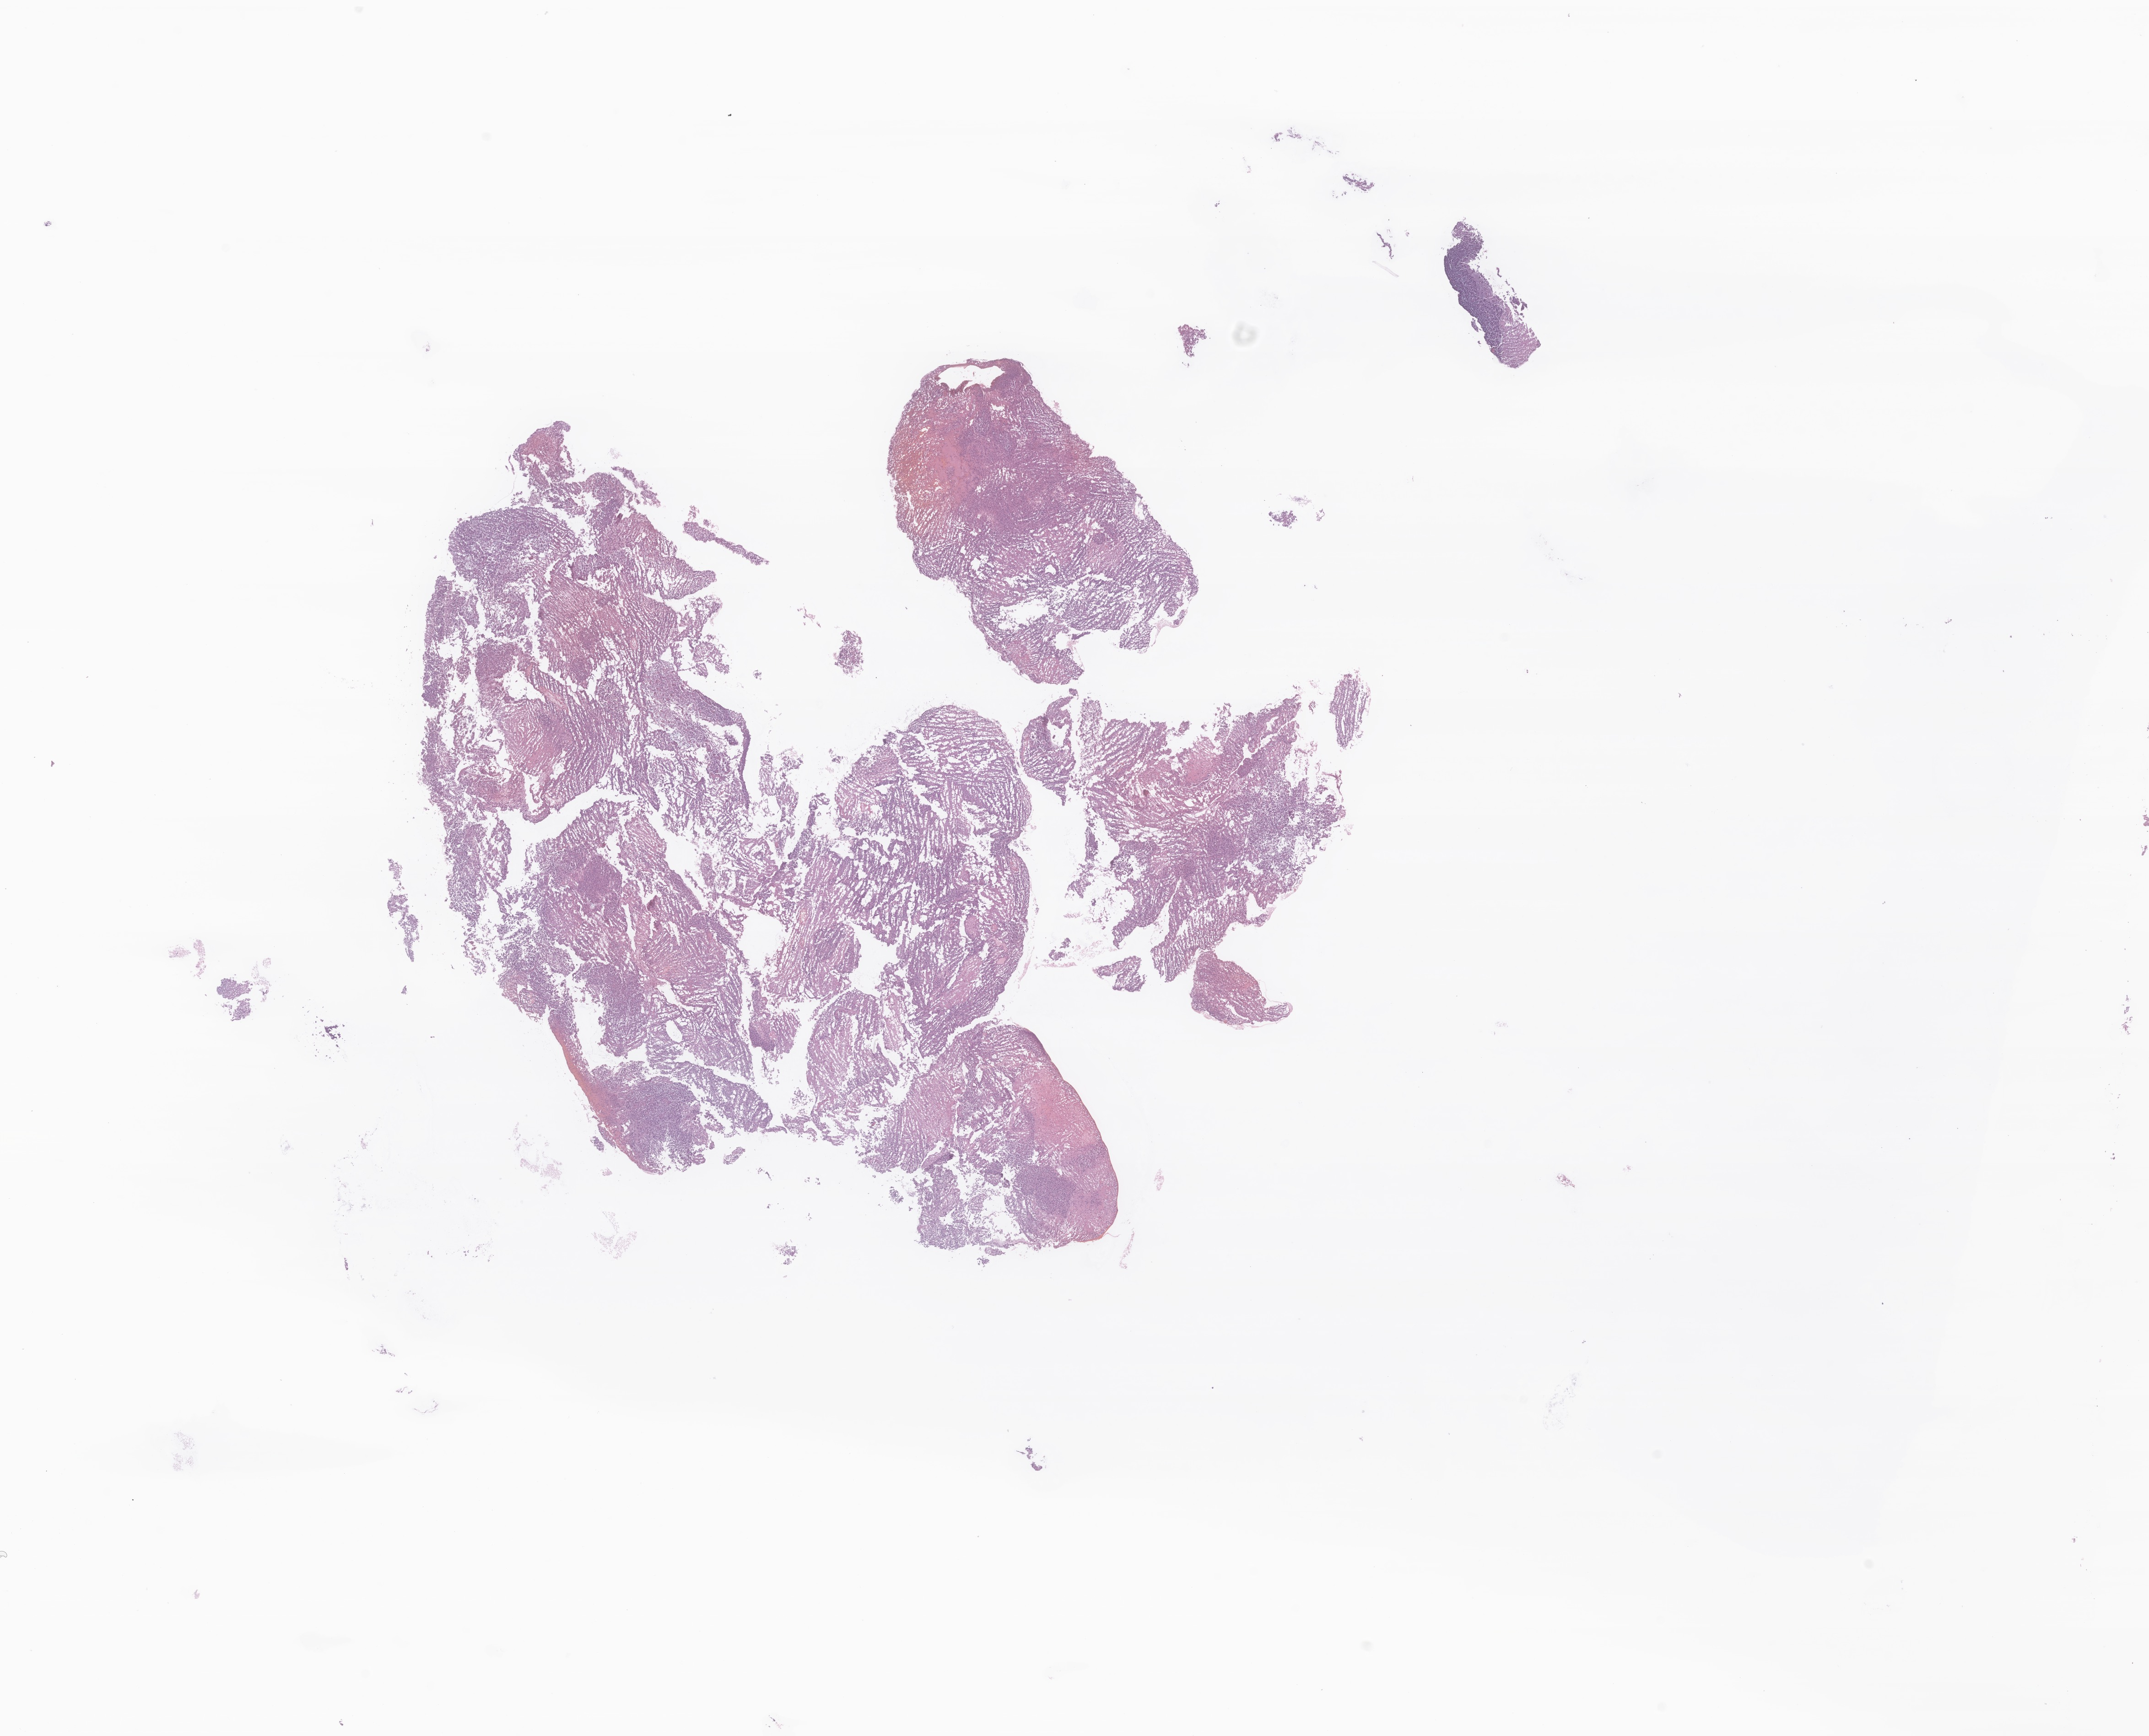
Hematoxylin and eosin (H&E) whole-slide image of tumor tissue from the spinal cord — a low-resolution overview of the entire scanned area, about 19.8 x 16.0 mm, formalin-fixed, paraffin-embedded (FFPE) tissue. Patient female; age 358 days.
Diagnosis (ICD-O-3 morphology term): Undifferentiated sarcoma.